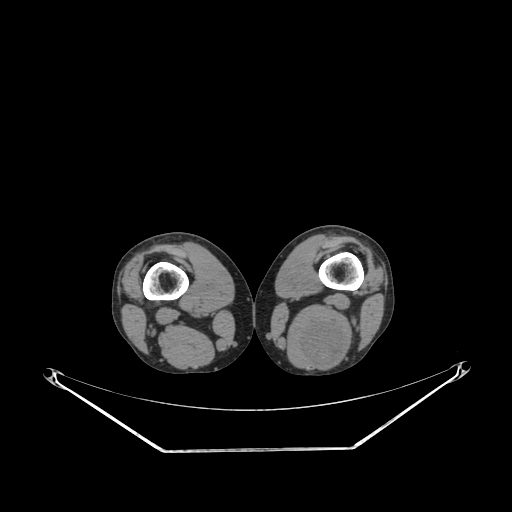
CT of an extremity soft-tissue mass (from a PET/CT study), one axial slice; position 197 of 267 along the scan axis; 140 kVp; soft-tissue window (W 400 / L 40 HU); 3.75 mm slice thickness; 512 × 512 image matrix, field of view 500 × 500 mm. Male patient. From the clinical record (not read from this slice): histological type: synovial sarcoma; site of the primary tumour: left poplietal fossa.
Outlined on this slice (expert contour drawn on MRI and transferred to this co-registered scan by the dataset authors):
- gross tumour volume (mass): bounding box <297,317,346,366> (left, top, right, bottom; pixels)